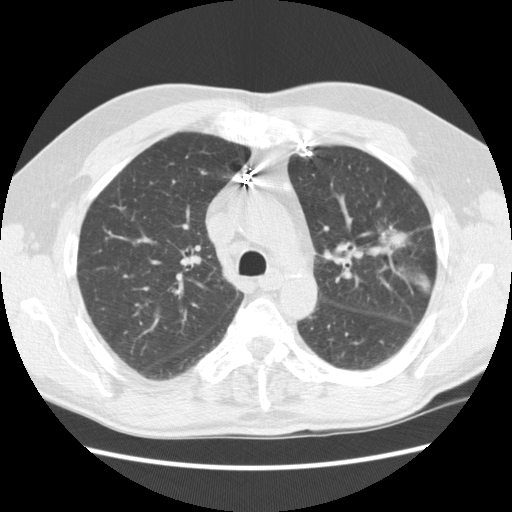
Low-dose screening chest CT, one axial slice; position 166 of 231 along the scan axis; 120 kVp; lung window (W 1500 / L -600 HU); 2.5 mm slice thickness; 512 × 512 image matrix, field of view 362 × 362 mm.
Structures marked on this image (outlined manually by an expert reader):
- lesion 1 (tumor, upper lobe of left lung): box from (x=389, y=232) to (x=408, y=245) px